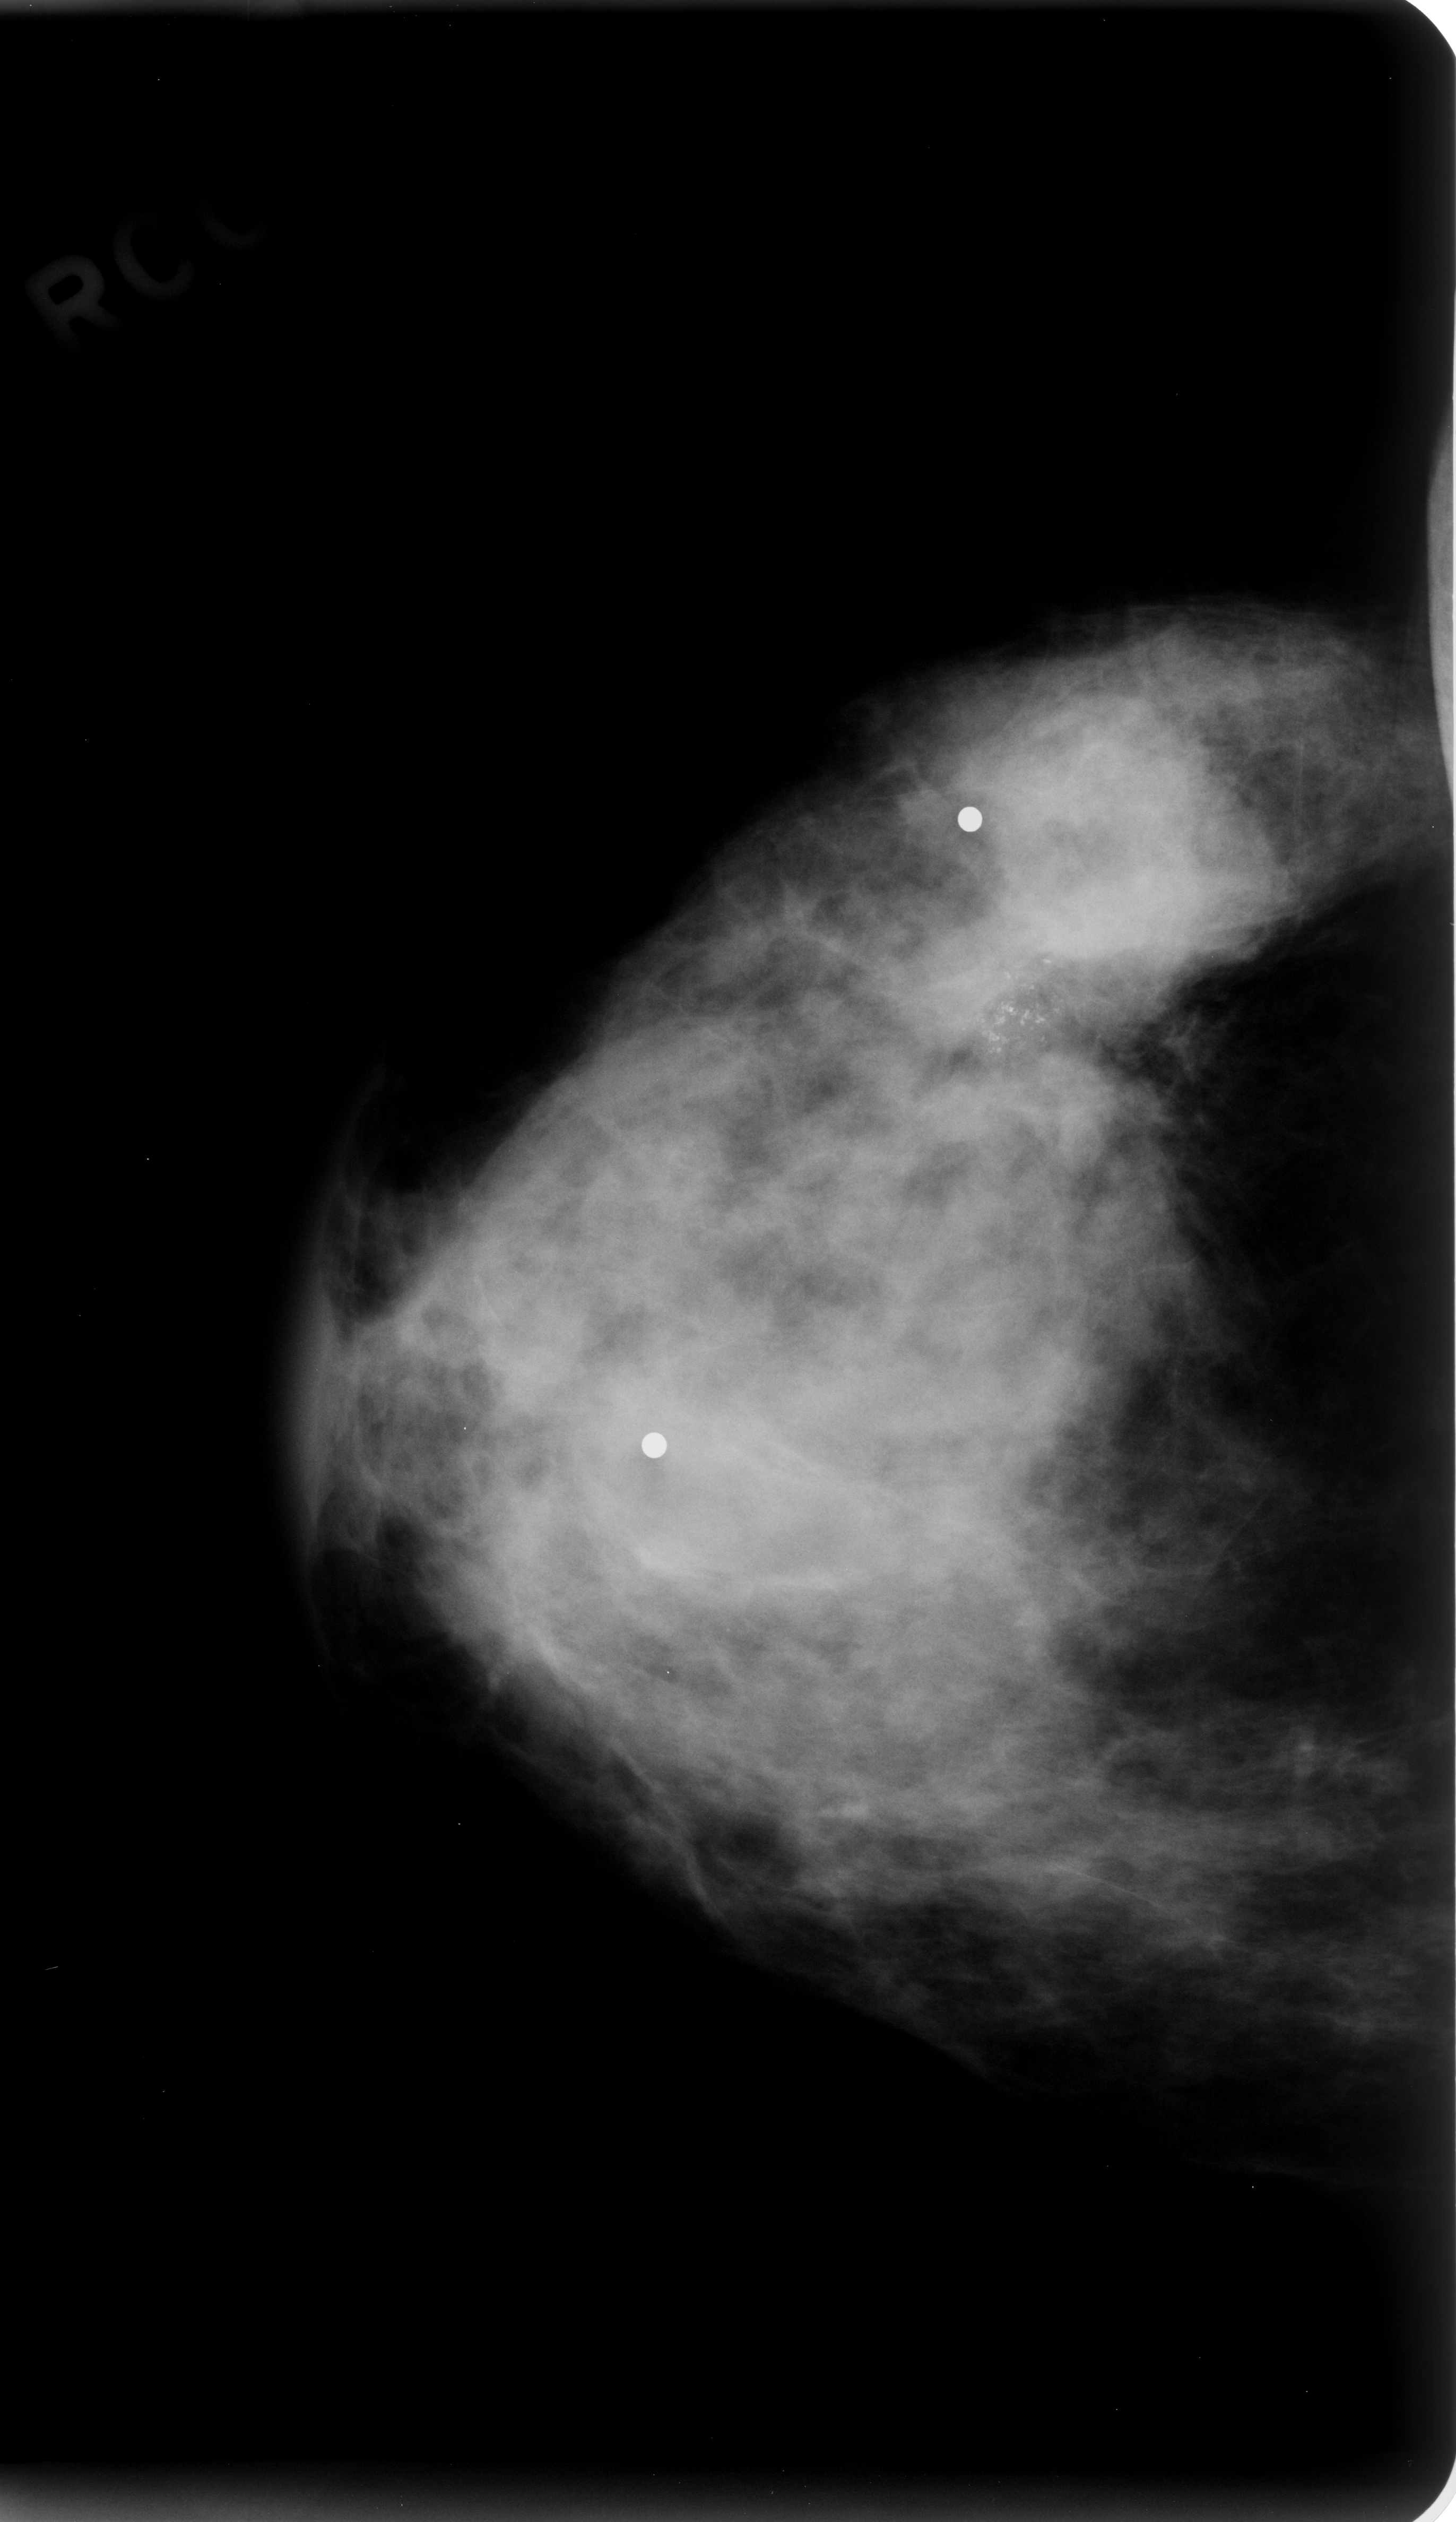
Mammogram (digitized film). Right breast. Craniocaudal (CC) view. BI-RADS breast density category 3 (scale 1–4). 1456 × 2522 image matrix.
Expert-marked regions of interest on this film, with their recorded descriptors:
- calcifications, morphology pleomorphic, distribution clustered; BI-RADS assessment category 5; subtlety rating 5 on a 1 (subtle) to 5 (obvious) scale; pathology (as recorded): malignant: bounding box <870,662,1274,1147> (left, top, right, bottom; pixels)